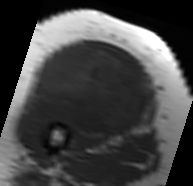
MRI of an extremity soft-tissue mass, one axial slice. Position 40 of 91 along the scan axis. MR volume resampled by the dataset authors to the PET/CT grid (not the native acquisition matrix). 3.27 mm slice thickness. 193 × 186 image matrix. Female patient. From the clinical record (not read from this slice): histological type: malignant solitary fibrous tumor; grade: intermediate; site of the primary tumour: right thigh.
Structures marked on this image (expert contour drawn on MRI and transferred to this co-registered scan by the dataset authors):
- gross tumour volume including surrounding oedema: bounding box [x1, y1, x2, y2] px = [24, 44, 153, 141]
- gross tumour volume (mass): [31, 44, 148, 138]